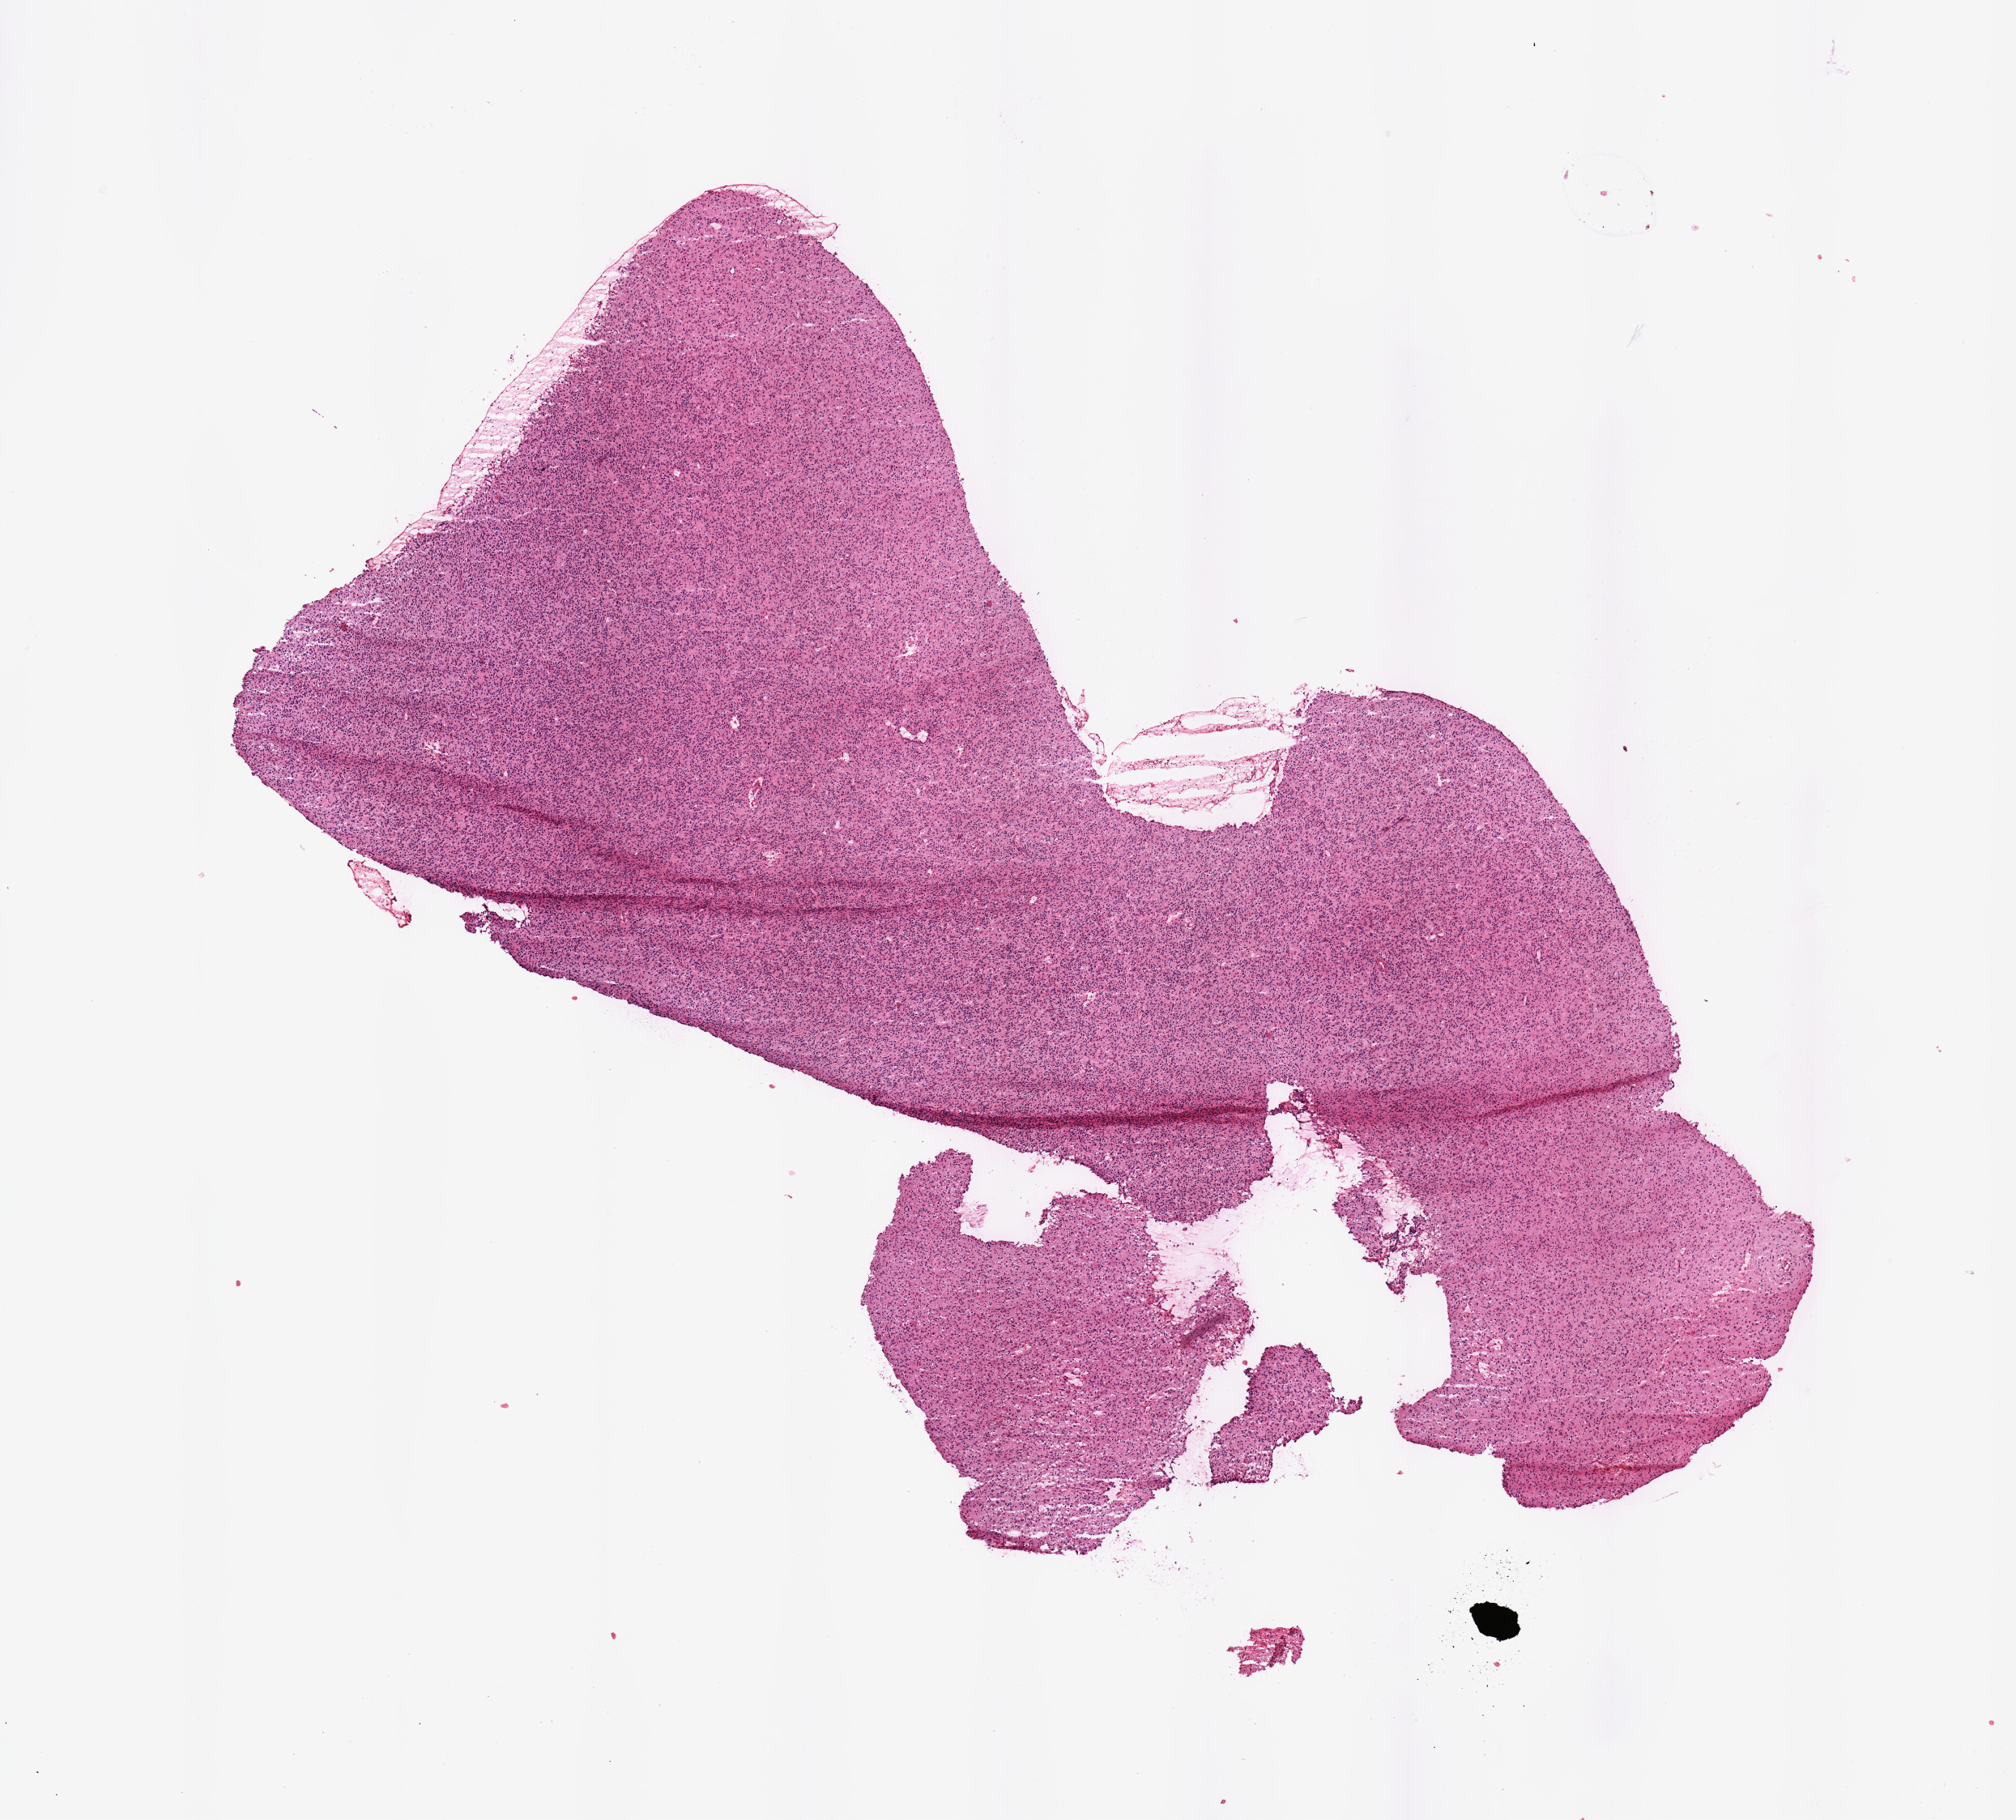
H&E whole-slide image — a low-resolution overview of the entire scanned area, about 9.8 x 8.9 mm; tumour tissue sample, brain. Female, 49 y/o.
Patient diagnosis (cohort enrolment): glioblastoma multiforme (brain). Primary tumour site (as recorded): parietal lobe.